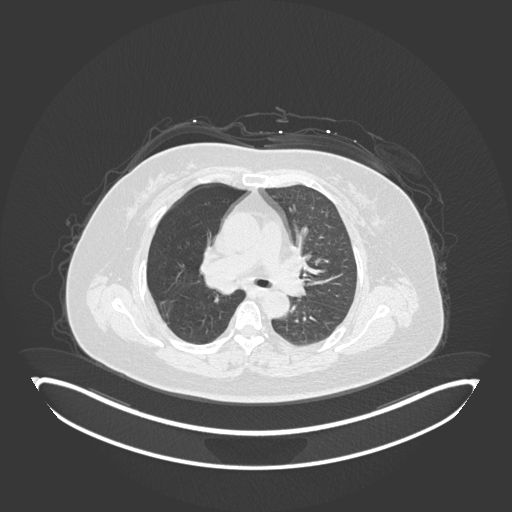
Chest CT, one axial slice; slice 103 of 245 in the series (ordered by position); reconstruction kernel B30f; 120 kVp; lung window (W 1500 / L -600 HU); 1 mm slice thickness; 512 × 512 image matrix, field of view 500 × 500 mm. Patient: female, 60 years. From the clinical record (not read from this slice): clinical TNM (as recorded): T1c N0 M0.
Structures marked on this image (bounding box drawn by a radiologist):
- lung tumour (recorded histology: squamous cell carcinoma): bounding box <203,268,239,296> (left, top, right, bottom; pixels)